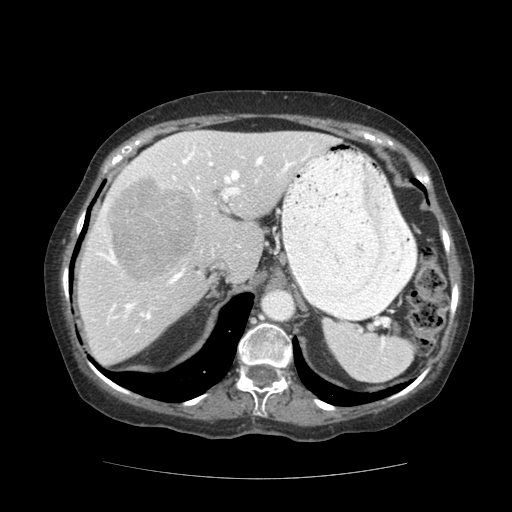
Contrast-enhanced abdominal CT (liver protocol), one axial slice; position 83 of 111 along the scan axis; 140 kVp; soft-tissue window (W 400 / L 40 HU); 2.5 mm slice thickness; 512 × 512 image matrix. From the clinical record (not read from this slice): diagnosis: hepatocellular carcinoma (patient treated with transarterial chemoembolisation; whether this scan precedes or follows treatment is not stated here); TNM stage (as recorded): Stage-I; Child-Pugh class: A; tumour differentiation: moderately-poorly differentiated.
Annotated regions visible in this slice (semi-automatically segmented with operator editing):
- liver parenchyma outside the tumour (the mass and vessels are separate outlines, so this box may not span the whole liver): bounding box [x1, y1, x2, y2] px = [78, 130, 332, 364]
- mass: [109, 179, 197, 278]
- liver vessels: [93, 136, 313, 332]